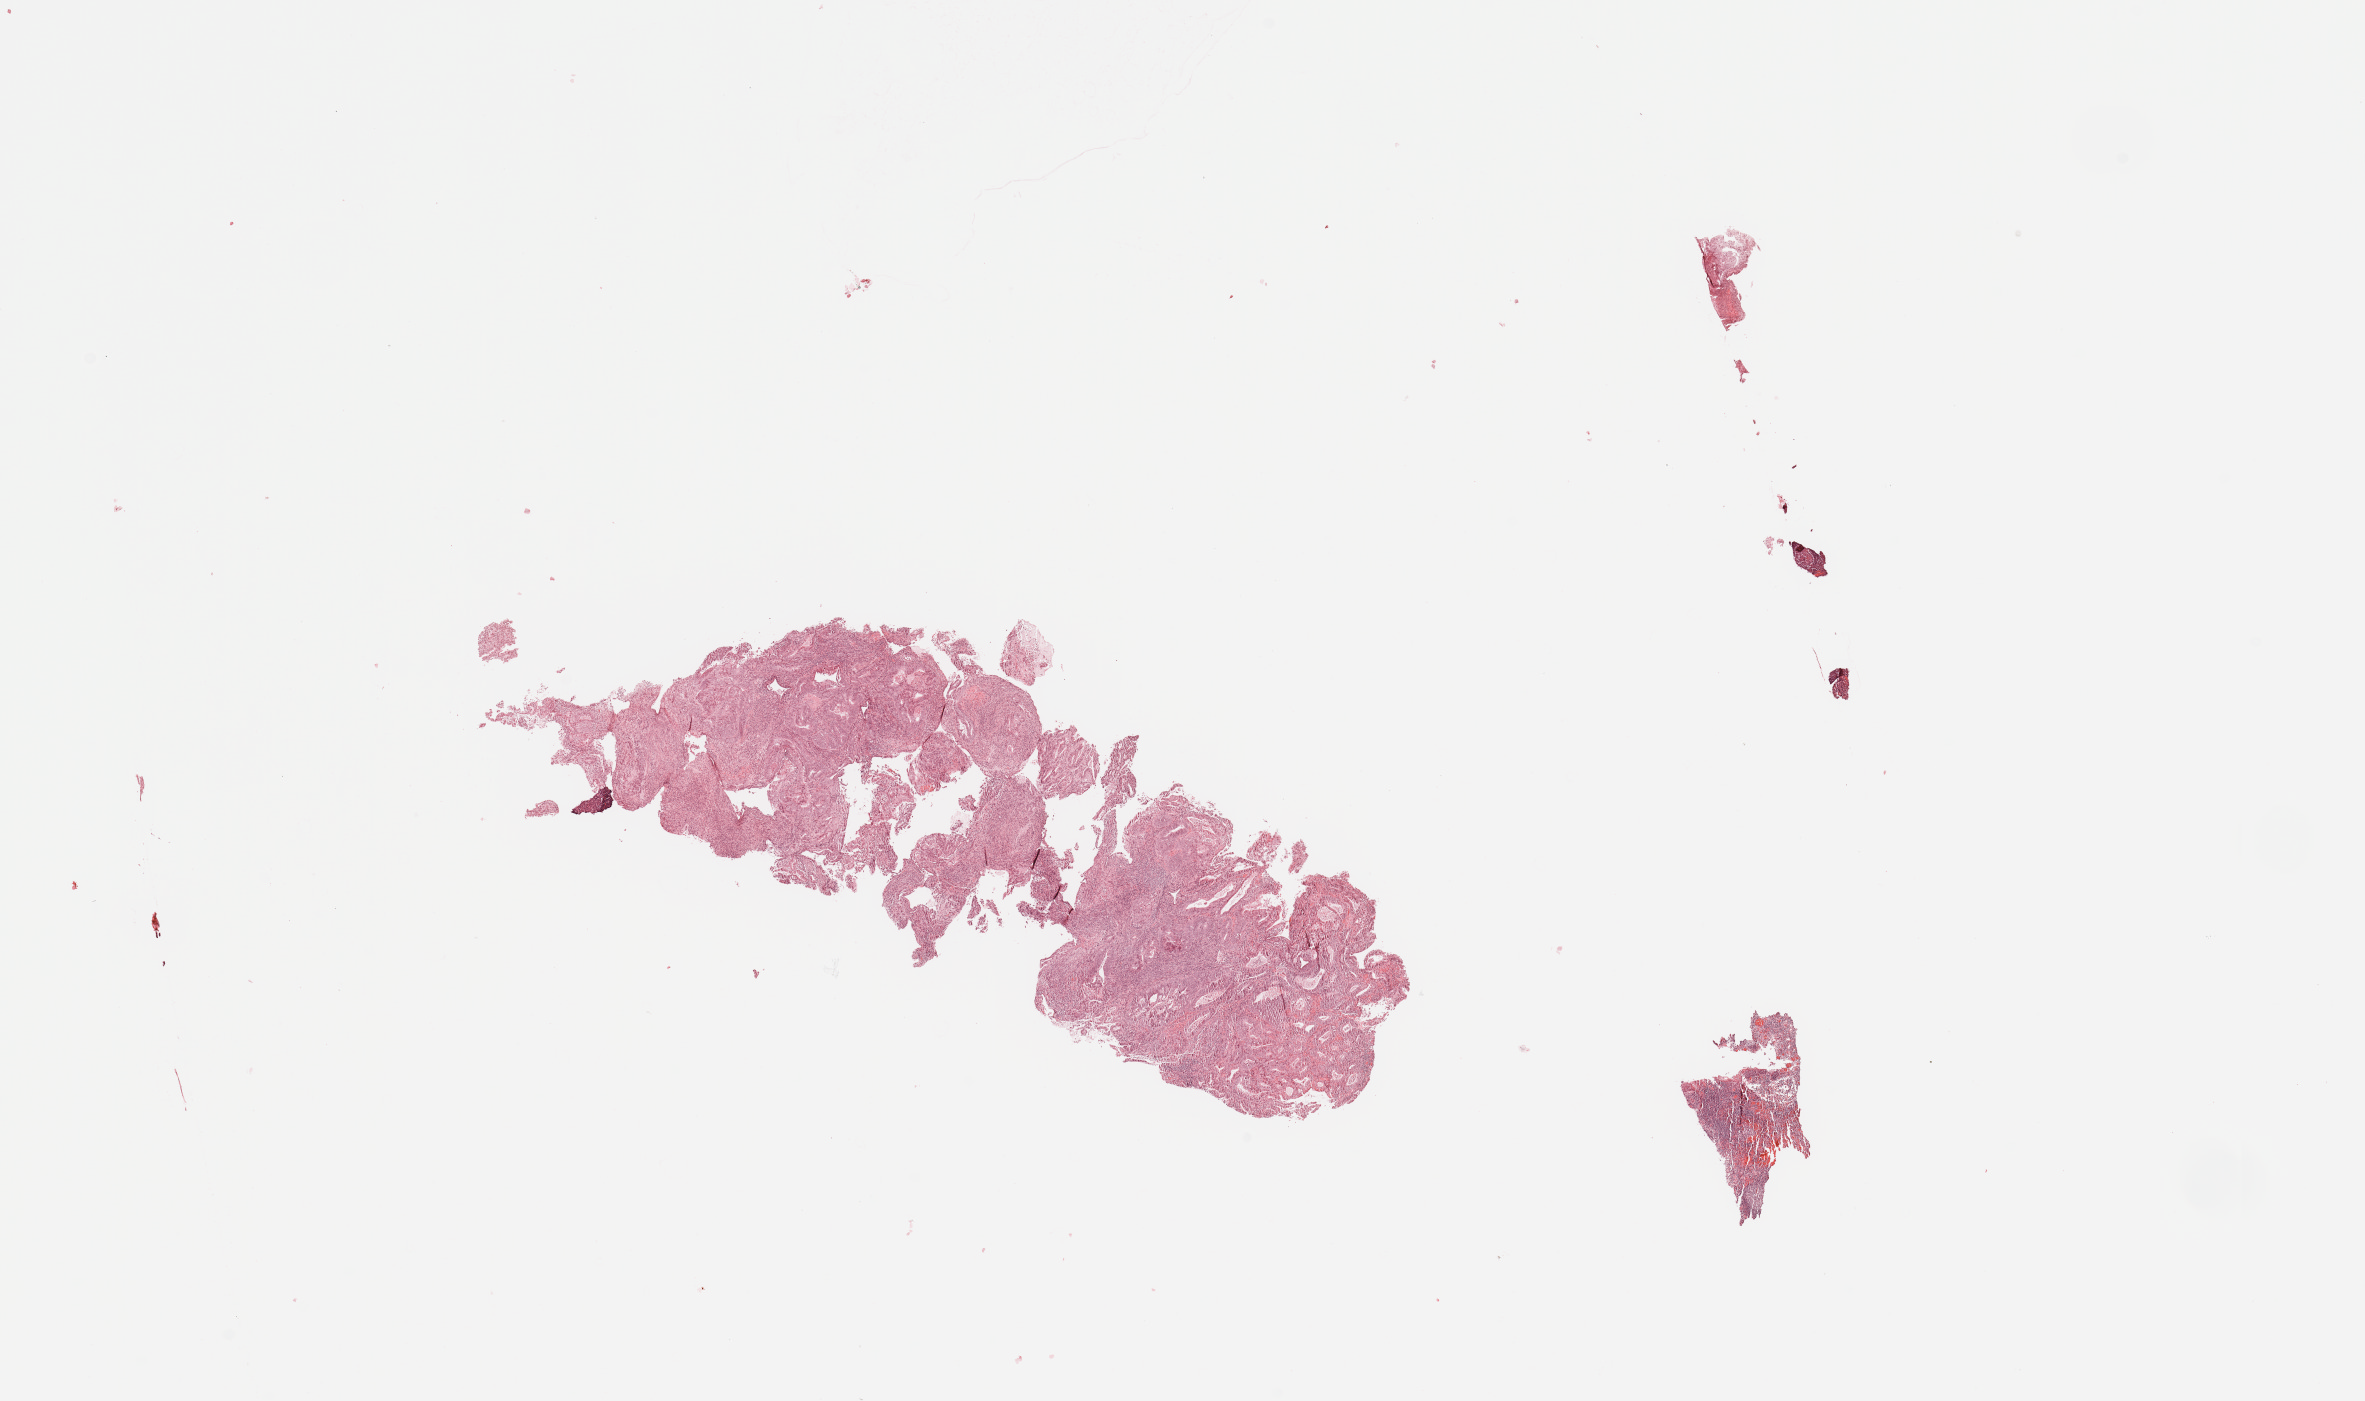
H&E-stained whole-slide image — a low-resolution overview of the entire scanned area, about 18.7 x 11.1 mm (acquisition: 20x scan), tumour tissue sample, sampled site: uterus. Female, 75 y/o. Histologic grade: G1 (well differentiated). Slide review estimates, as recorded: tumour nuclei 80%, necrosis 1%.
- AJCC pathologic stage: I
- diagnosis: Endometrioid adenocarcinoma, NOS
- primary tumour site (as recorded): anterior endometrium